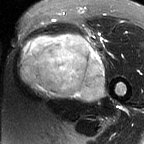
MRI of an extremity soft-tissue mass, one axial slice; slice 38 of 60 in the series (ordered by position); T2-weighted fat-saturated; MR volume resampled by the dataset authors to the PET/CT grid (not the native acquisition matrix); 3.27 mm slice thickness; 144 × 144 image matrix, field of view 141 × 141 mm. Female patient. Case-level facts recorded for this patient, not image findings: histological type: pleiomorphic leiomyosarcoma; grade: intermediate; site of the primary tumour: left thigh.
Outlined on this slice (expert contour drawn on MRI and transferred to this co-registered scan by the dataset authors):
- gross tumour volume including surrounding oedema: box from (x=18, y=33) to (x=105, y=102) px
- gross tumour volume (mass): (x=18, y=33)–(x=105, y=100)